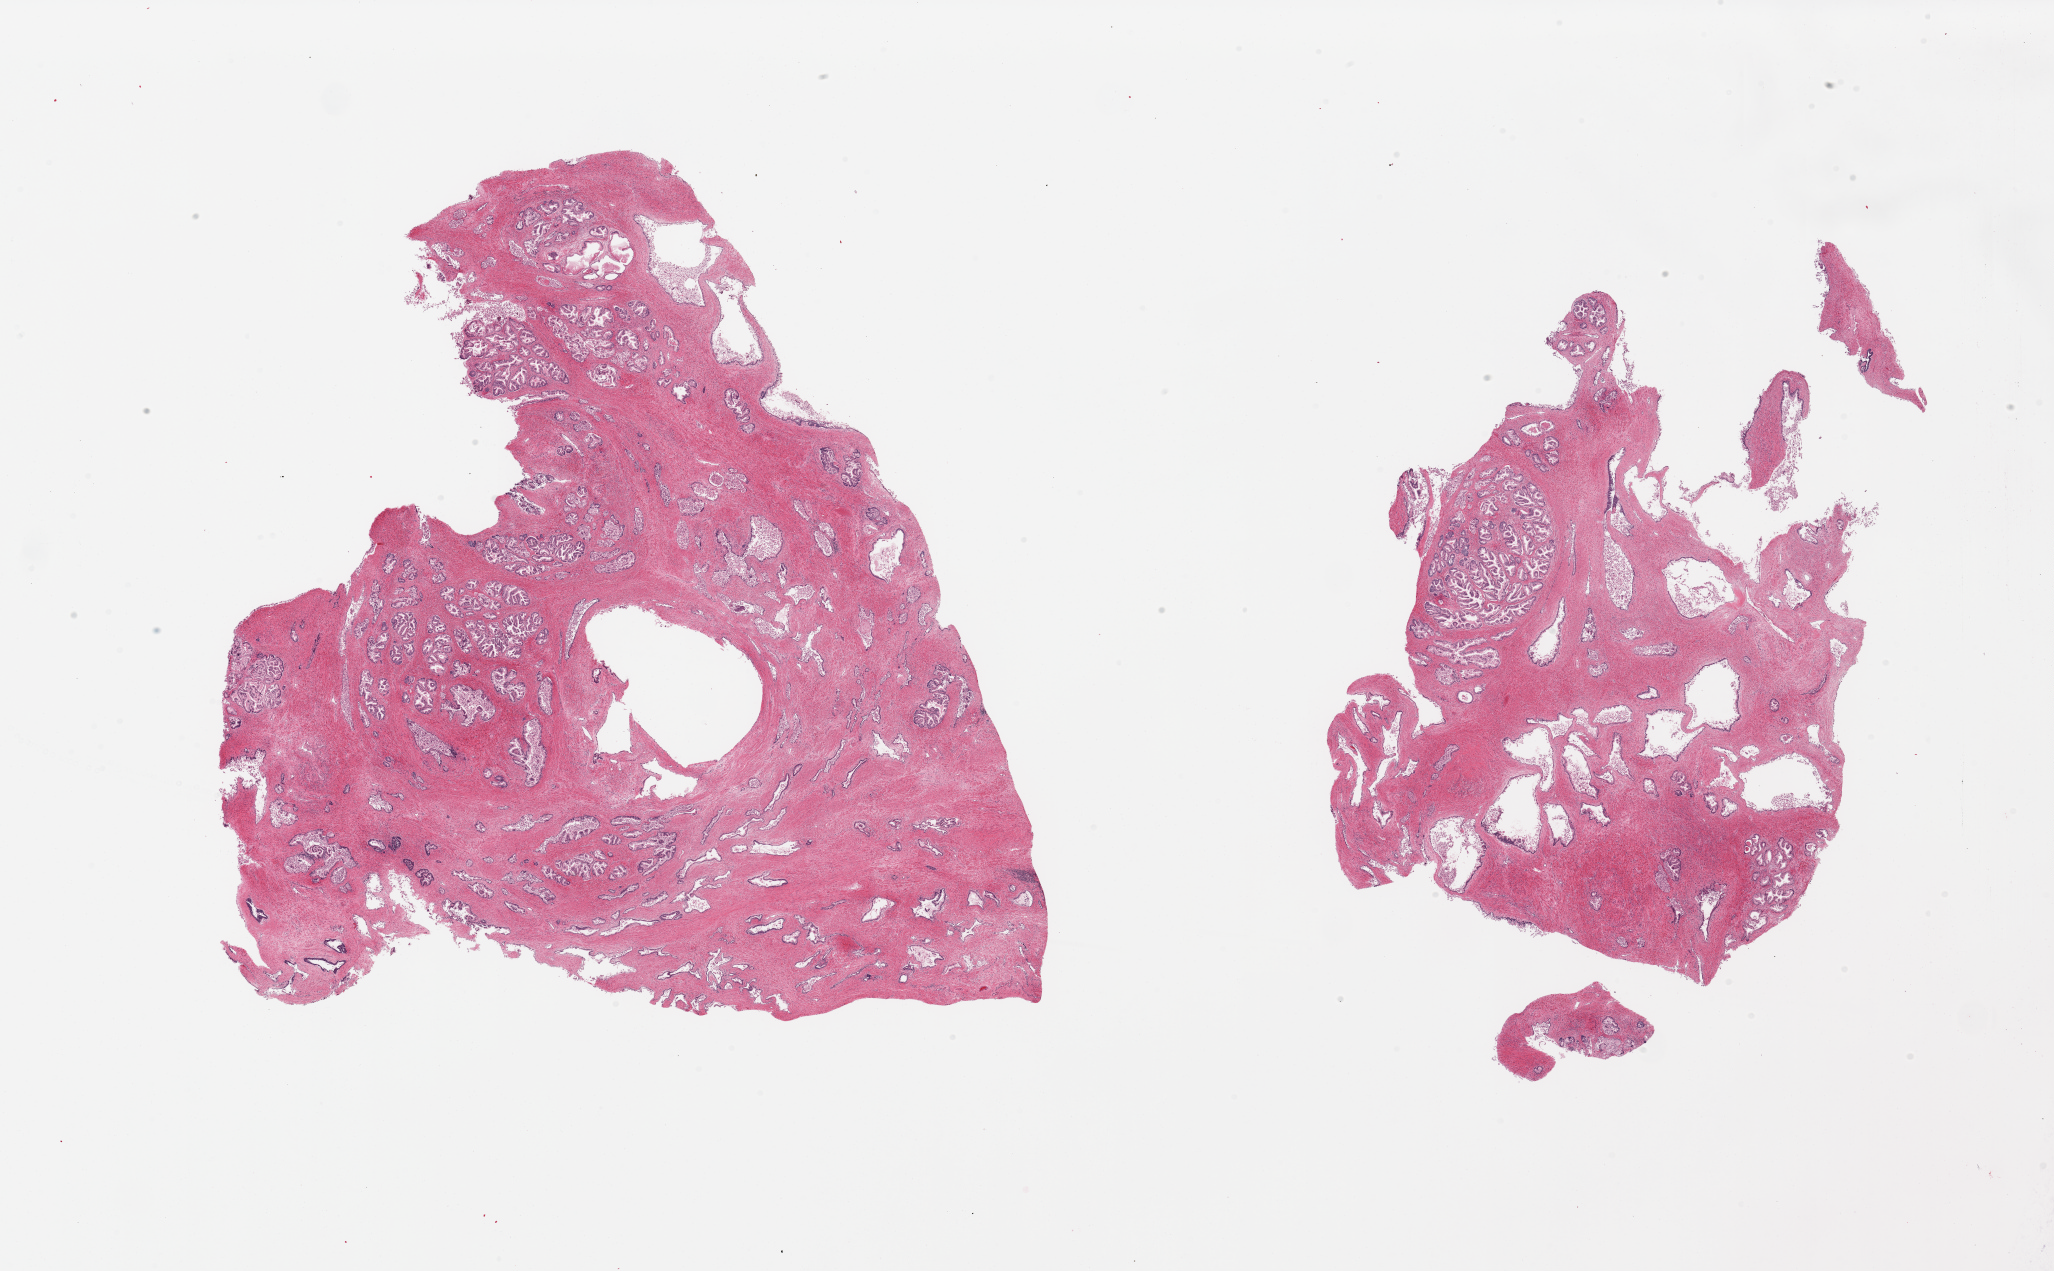
Whole-slide image, haematoxylin and eosin stain, shown as a low-resolution overview of the whole scanned area (about 32.5 x 20.1 mm); PAXgene-fixed paraffin-embedded (PFPE) section; target tissue: prostate; donor tissue sample. Donor sex: male.
Pathologist's review note for this sample: 2 pieces, glandular hyperplasia.